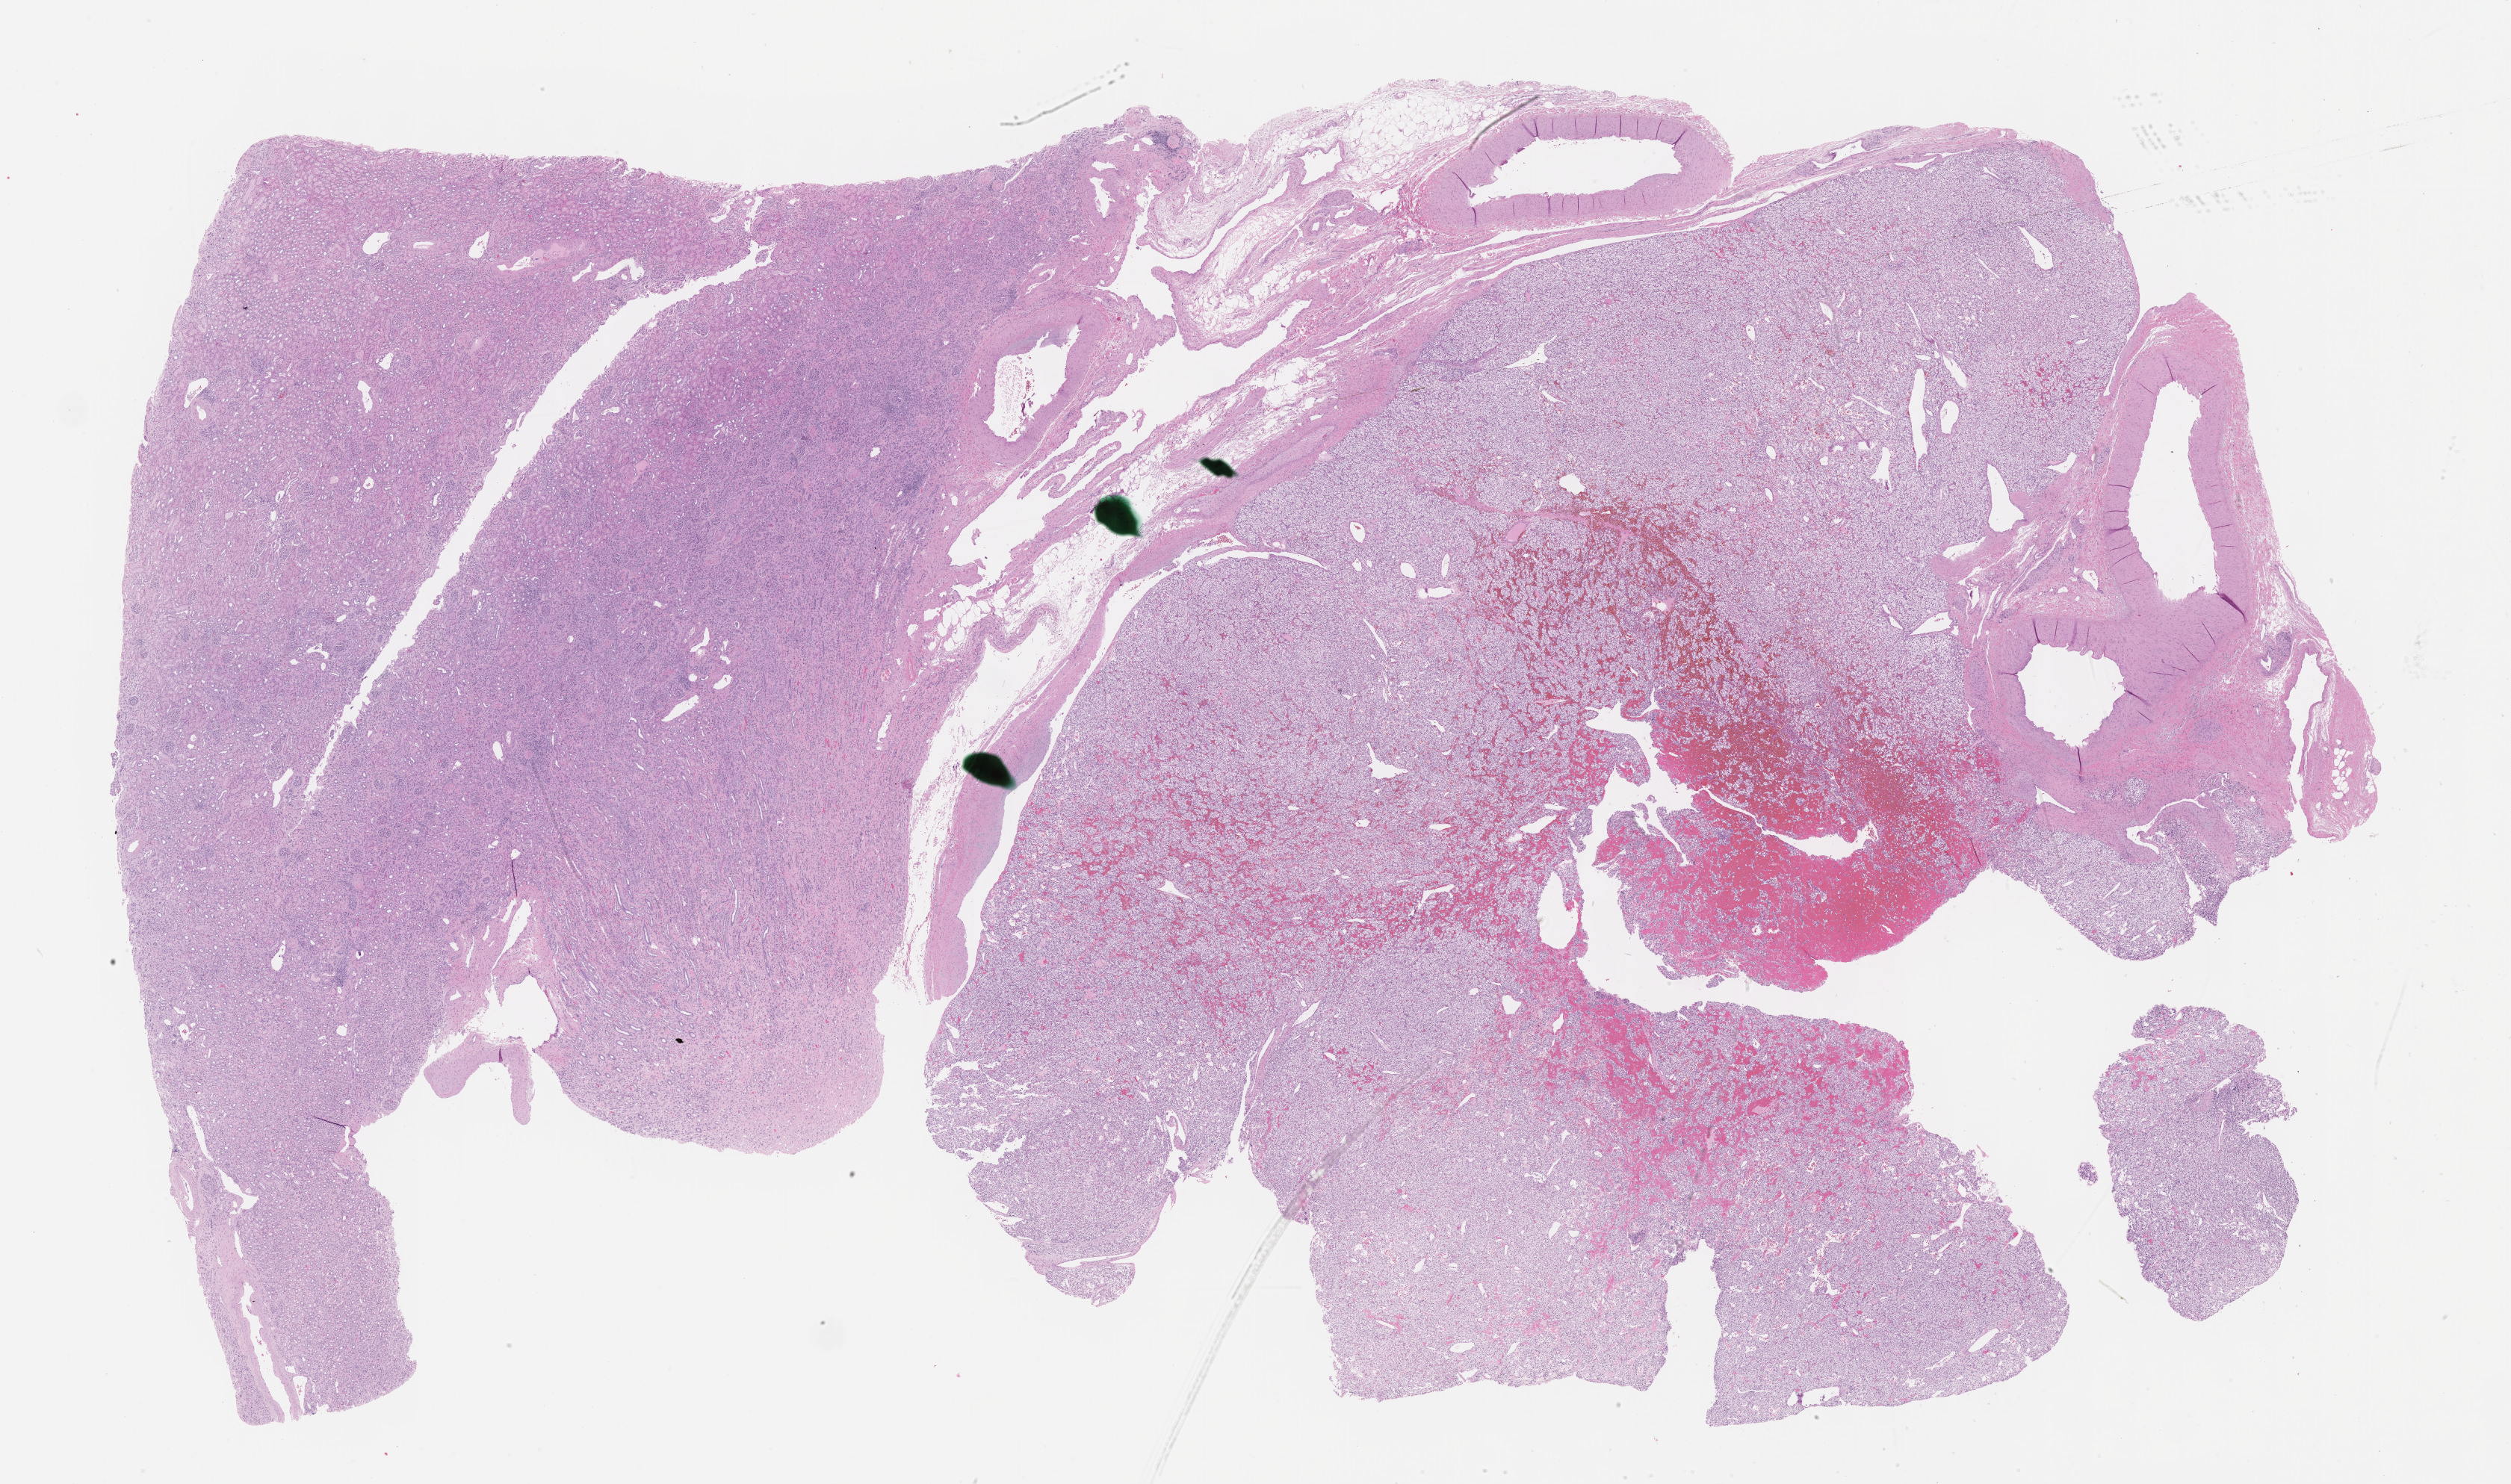
Digitized H&E-stained tissue section (whole slide), whole scanned area (about 27.2 x 16.1 mm, from a 40x scan) shown as a low-resolution overview. Formalin-fixed paraffin-embedded (FFPE) diagnostic section. Kidney, primary tumour sample. Female patient; age at initial diagnosis 60 years.
Histologic diagnosis: Clear cell adenocarcinoma, NOS.